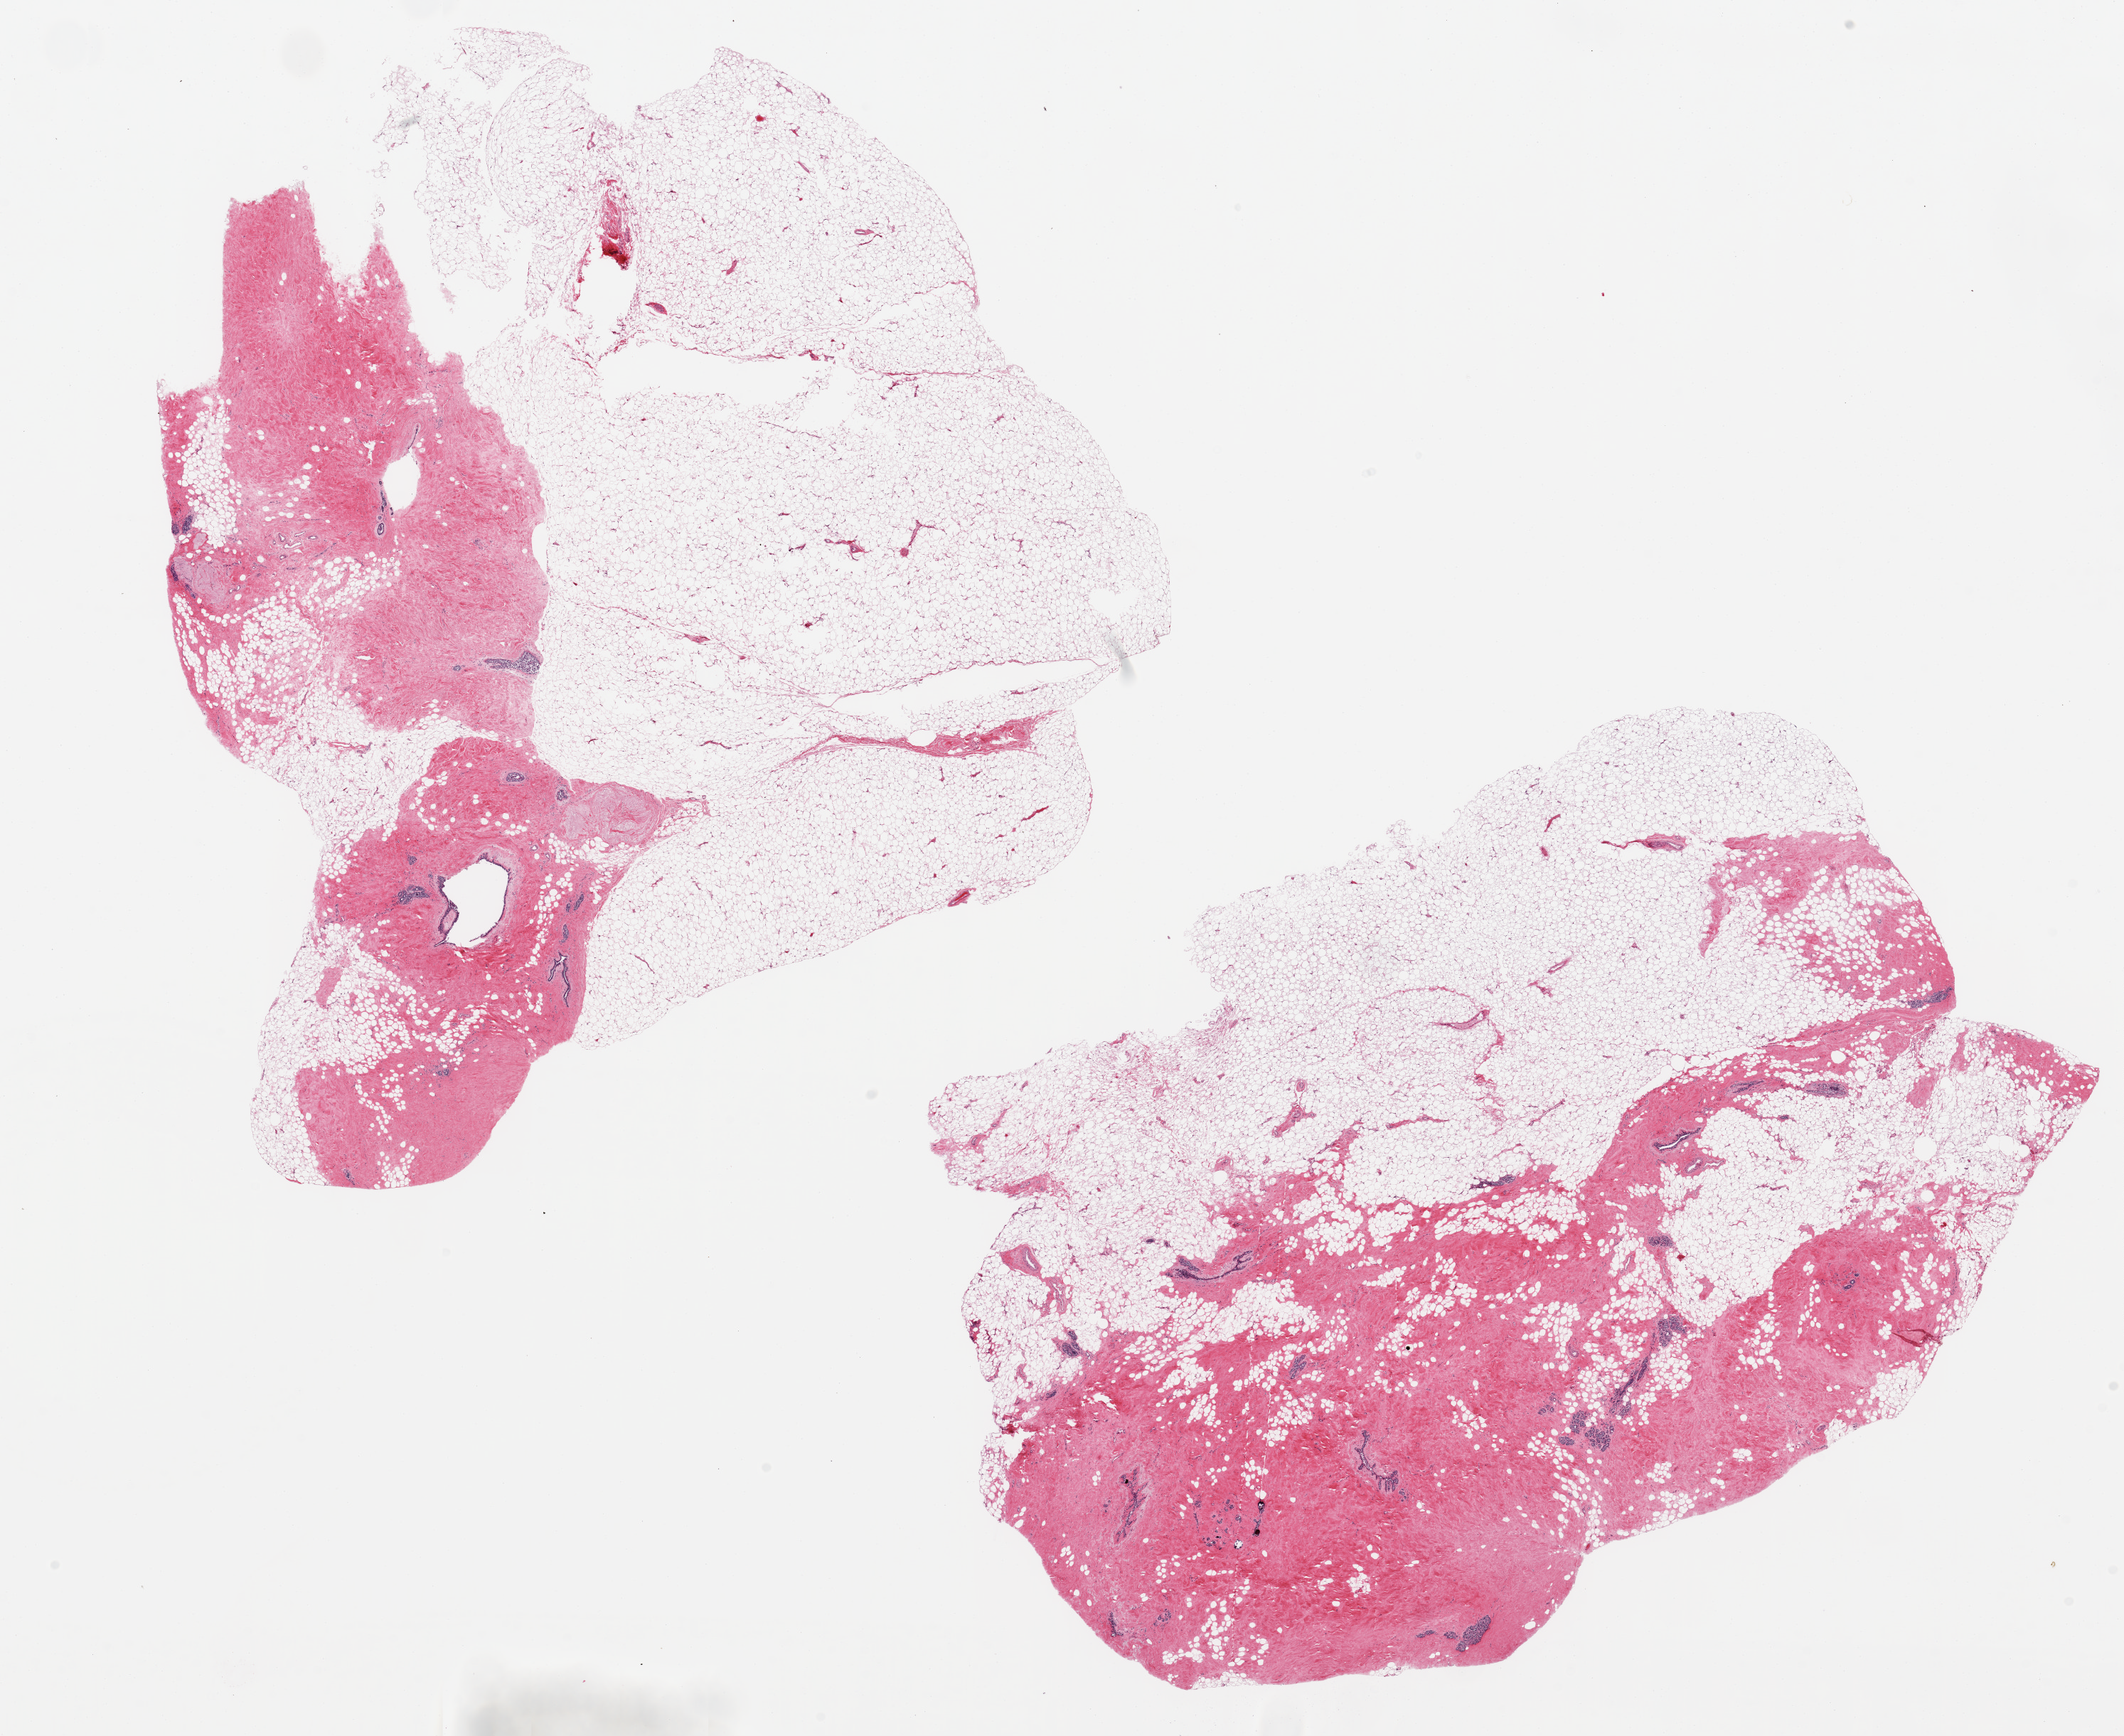
Whole-slide image, haematoxylin and eosin stain — whole scanned area (about 23.6 x 19.3 mm) shown as a low-resolution overview. PAXgene-fixed, paraffin-embedded tissue. Sampled site (target tissue): breast. Donor tissue sample. Female donor.
Reviewer comment on this tissue sample: 2 11x9mm aliquots. Atrophic mammary ductal and lobular elements noted.